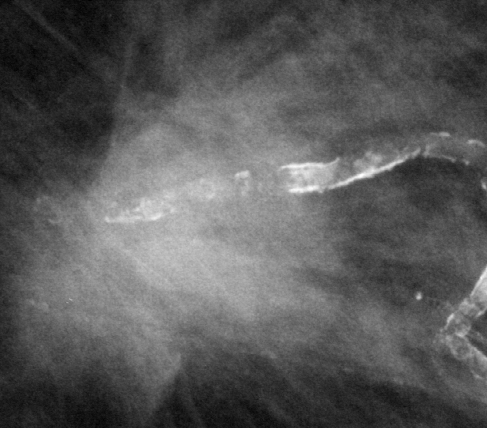
Crop from a digitized film mammogram around one marked abnormality, left breast, CC view, BI-RADS breast density category 2 (scale 1–4).
- Mass, shape oval, margins spiculated; BI-RADS assessment category 5; pathology (as recorded): malignant.